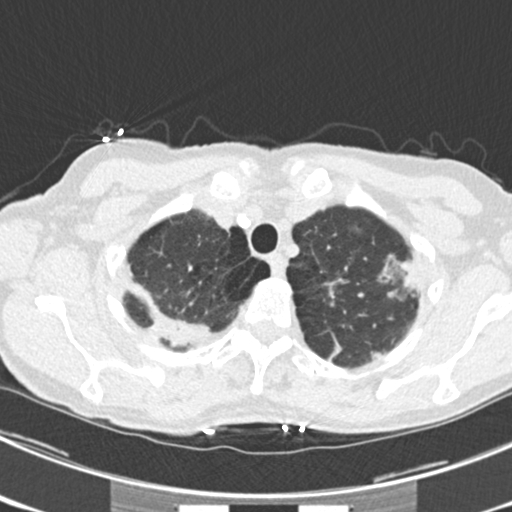
Axial slice from a low-dose chest CT screening exam; third screening round (two years after baseline); lung window (W 1500 / L -600 HU); 2 mm slice thickness; slice 38 of 225 in the series; 512 × 512 image matrix. Female participant, aged 63 years at enrolment. Current smoker at enrolment.
• Expert-annotated lung lesion, bounding box (x1, y1, x2, y2) in pixels: (372, 244, 437, 307).
• The screening reader recorded 9 non-calcified nodules or masses ≥4 mm on this exam (left upper lobe, right upper lobe, left upper lobe, left lower lobe, right middle lobe, left lower lobe, left lower lobe, right lower lobe, right lower lobe); which of them this box marks is not recorded.
• Official screen result: positive, other.
• Later outcome: lung cancer diagnosed 15 days after this screen — bronchiolo-alveolar adenocarcinoma, NOS, right upper lobe, right middle lobe, right lower lobe, left upper lobe, left lower lobe, moderately differentiated (G2), stage IV (AJCC 6th edition).